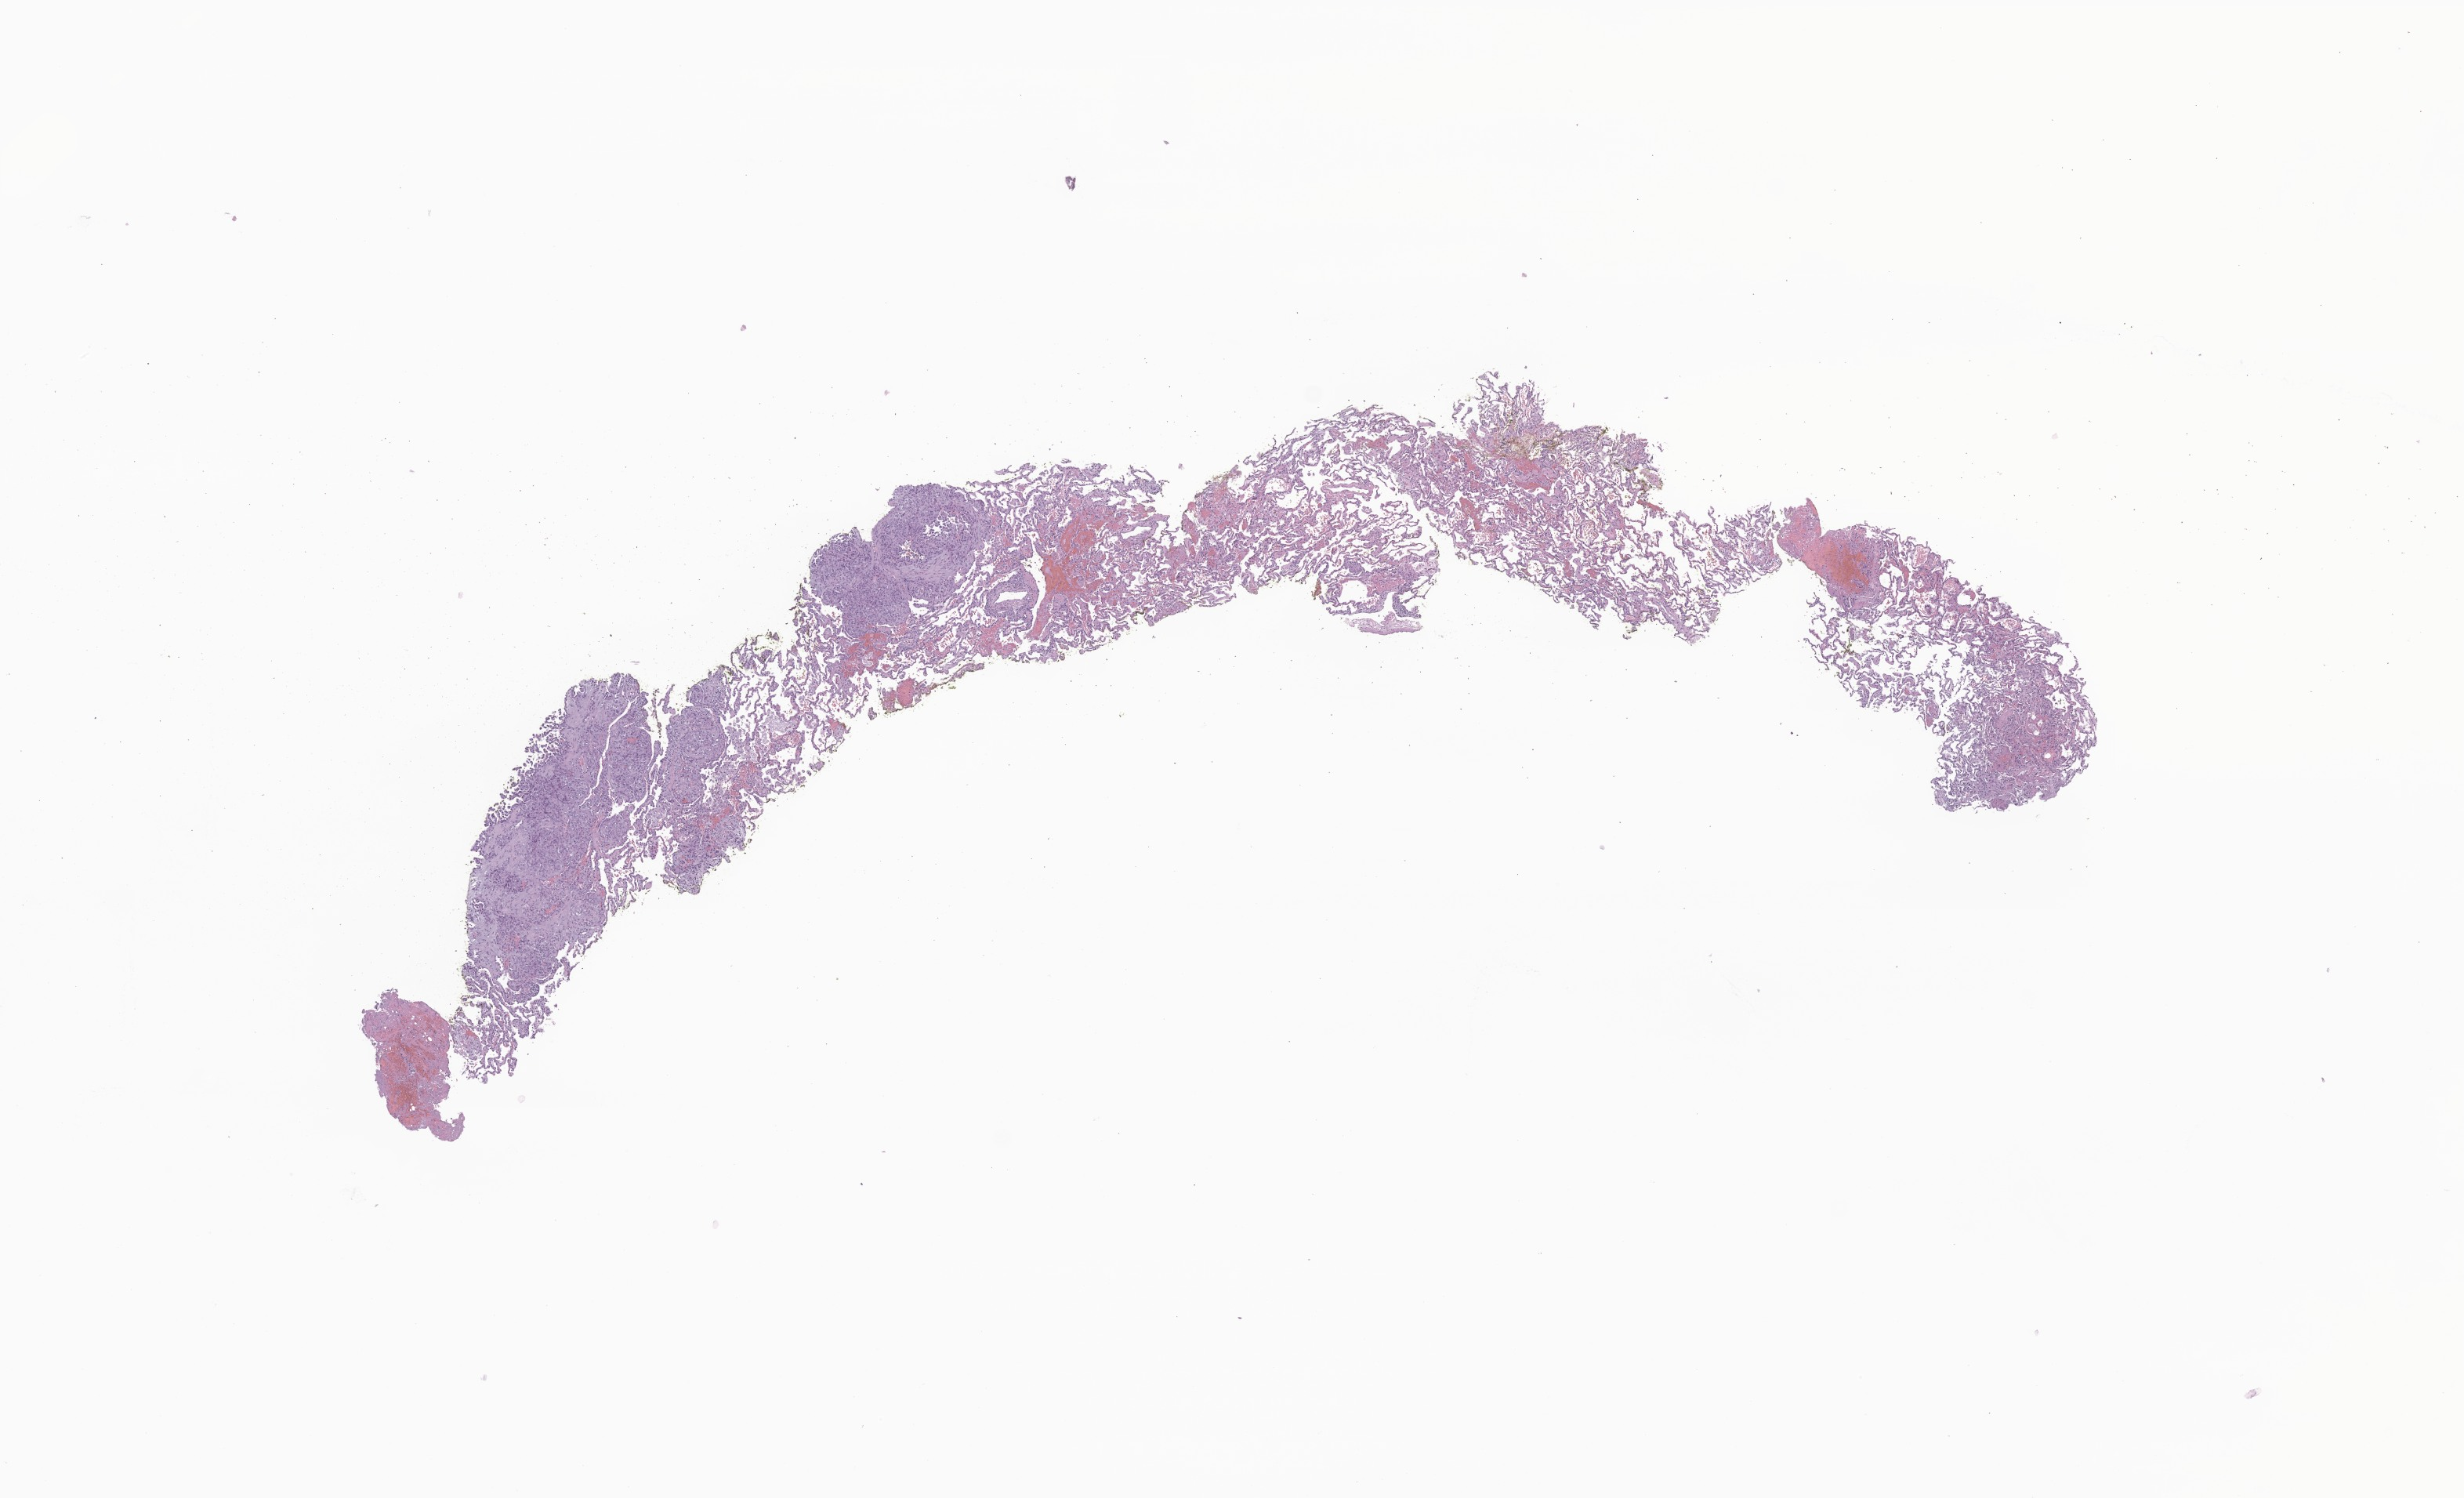
Whole-slide image, H&E stain of tumor tissue from the peritoneum — low-resolution overview of the scanned area, about 13.3 x 8.1 mm. Formalin-fixed, paraffin-embedded (FFPE) tissue. Patient: male, age 205 months (17 years 1 month).
Diagnosis (ICD-O-3 morphology term): Malignant peripheral nerve sheath tumor, NOS.